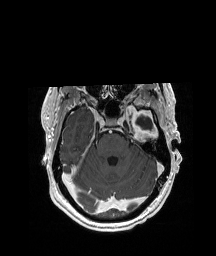
Brain MRI from a brain-tumour surgery series, one axial slice. Position 139 of 208 along the scan axis. T1-weighted post-contrast. 216 × 256 image matrix, field of view 228 × 270 mm. Case-level facts recorded for this patient, not image findings: histopathology: Glioblastoma; WHO grade: 4; IDH mutation: no; tumour location: Left Anterior/Superior Temporal.
Annotated regions visible in this slice (outlined manually by an expert reader):
- previous resection cavity: box from (x=135, y=116) to (x=154, y=132) px
- tumour: (x=123, y=101)–(x=158, y=138)